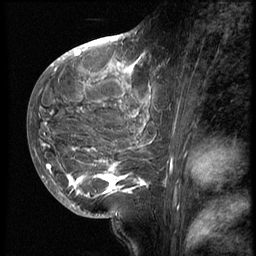
Breast MRI (dynamic contrast-enhanced), one sagittal slice; position 25 of 62 along the scan axis; 3 images stored at this slice position (order not interpretable as contrast timing); 1.5 T; TE 4.2 ms, TR 9 ms; 256 × 256 image matrix, field of view 180 × 180 mm. Female patient, age 28 years. From the clinical record (not read from this slice): setting: breast cancer imaged before/during neoadjuvant chemotherapy.
Structures marked on this image (semi-automatically segmented with operator editing):
- analysis volume of interest (the breast-tissue region the enhancement analysis was run in; not a lesion): bounding box <42,45,165,207> (left, top, right, bottom; pixels)
- tumour enhancement mask (voxels above the 140 % enhancement threshold inside the analysis volume of interest): <42,50,152,198>